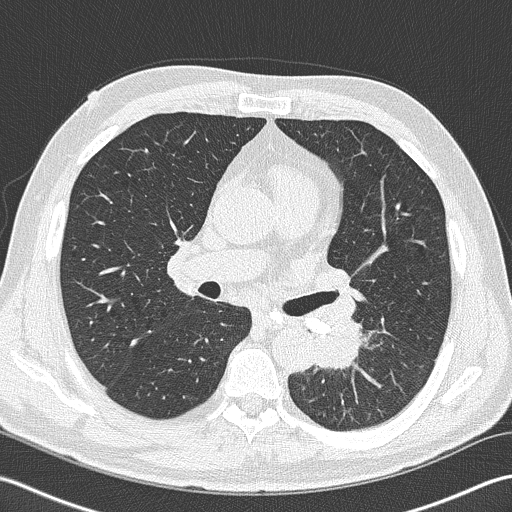
Axial slice from a low-dose chest CT screening exam, second screening round (one year after baseline), lung window (W 1500 / L -600 HU), lung (sharp) reconstruction kernel (B50f), 120 kVp. Male, age 57 years at enrolment.
Lesion marked by an expert reader, bounding box [x1, y1, x2, y2] px = [293, 304, 373, 382]. Screening reader's record for this exam (one nodule recorded; not confirmed to be the boxed lesion): non-calcified nodule or mass ≥4 mm, left lower lobe, 40 × 30 mm, spiculated (stellate) margins, soft tissue attenuation, pre-existing on the prior screen: no. Later outcome: lung cancer diagnosed 9 days after this screen — squamous cell carcinoma, NOS, left lower lobe, moderately differentiated (G2), stage IIIB (AJCC 6th edition), 38 mm at pathology.